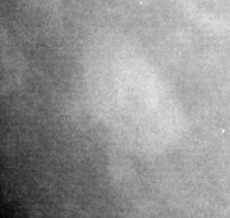
Region of interest cut from a scanned film mammogram (one marked finding), right breast, MLO view, BI-RADS breast density category 1 (scale 1–4).
- Marked abnormality: mass, shape oval / lymph node, margins circumscribed; BI-RADS assessment category 2; subtlety rating 4 on a 1 (subtle) to 5 (obvious) scale; benign; no additional work-up was recommended (benign without callback).